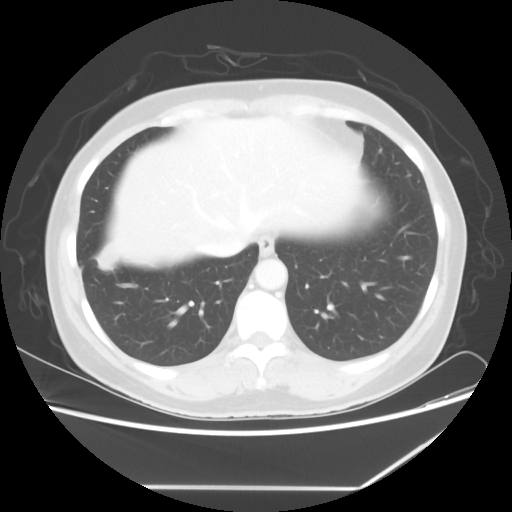
Chest CT, one axial slice. Slice 17 of 60 in the series (ordered by position). Reconstruction kernel STANDARD. Lung window (W 1500 / L -600 HU). 5 mm slice thickness. 512 × 512 image matrix, field of view 374 × 374 mm. Female patient, age 42 years. Case-level facts recorded for this patient, not image findings: clinical TNM (as recorded): T2 N1 M0.
Outlined on this slice (bounding box drawn by a radiologist):
- lung tumour (recorded histology: adenocarcinoma): bounding box <93,240,123,271> (left, top, right, bottom; pixels)